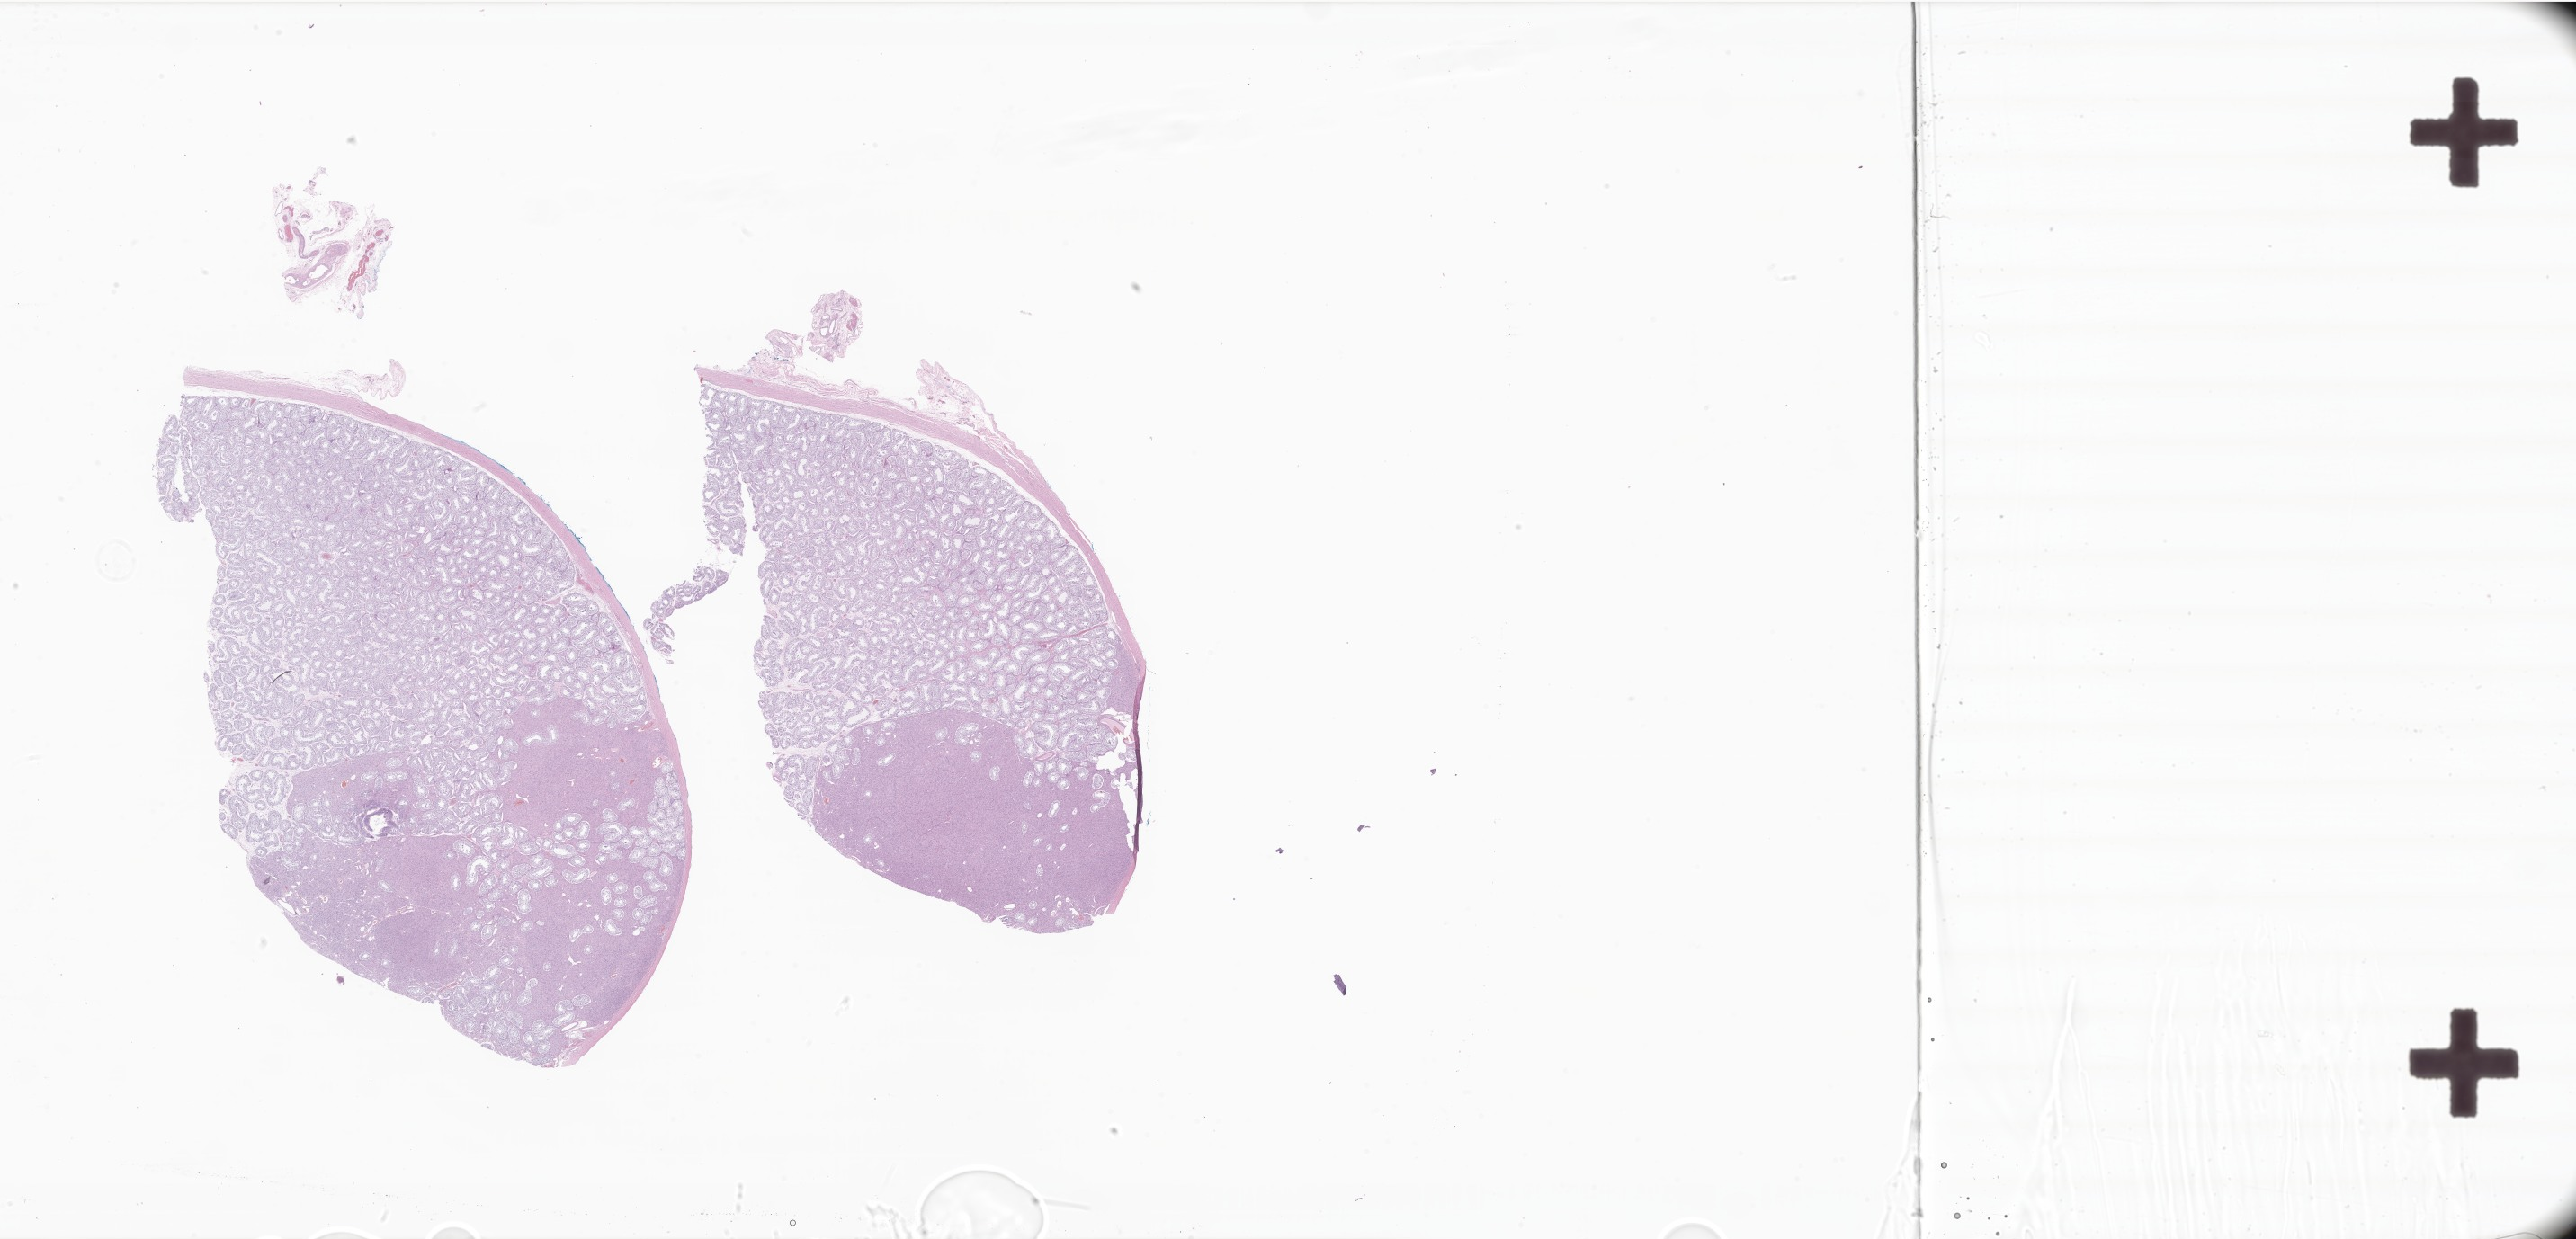
Whole-slide image, haematoxylin and eosin stain of tumor tissue from the testis — a low-resolution overview of the entire scanned area, about 48.3 x 23.2 mm; formalin-fixed, paraffin-embedded (FFPE) tissue. Patient: male, age 103 months (8 years 7 months).
- diagnosis (ICD-O-3 morphology term): Leydig cell tumor of ovary, NOS